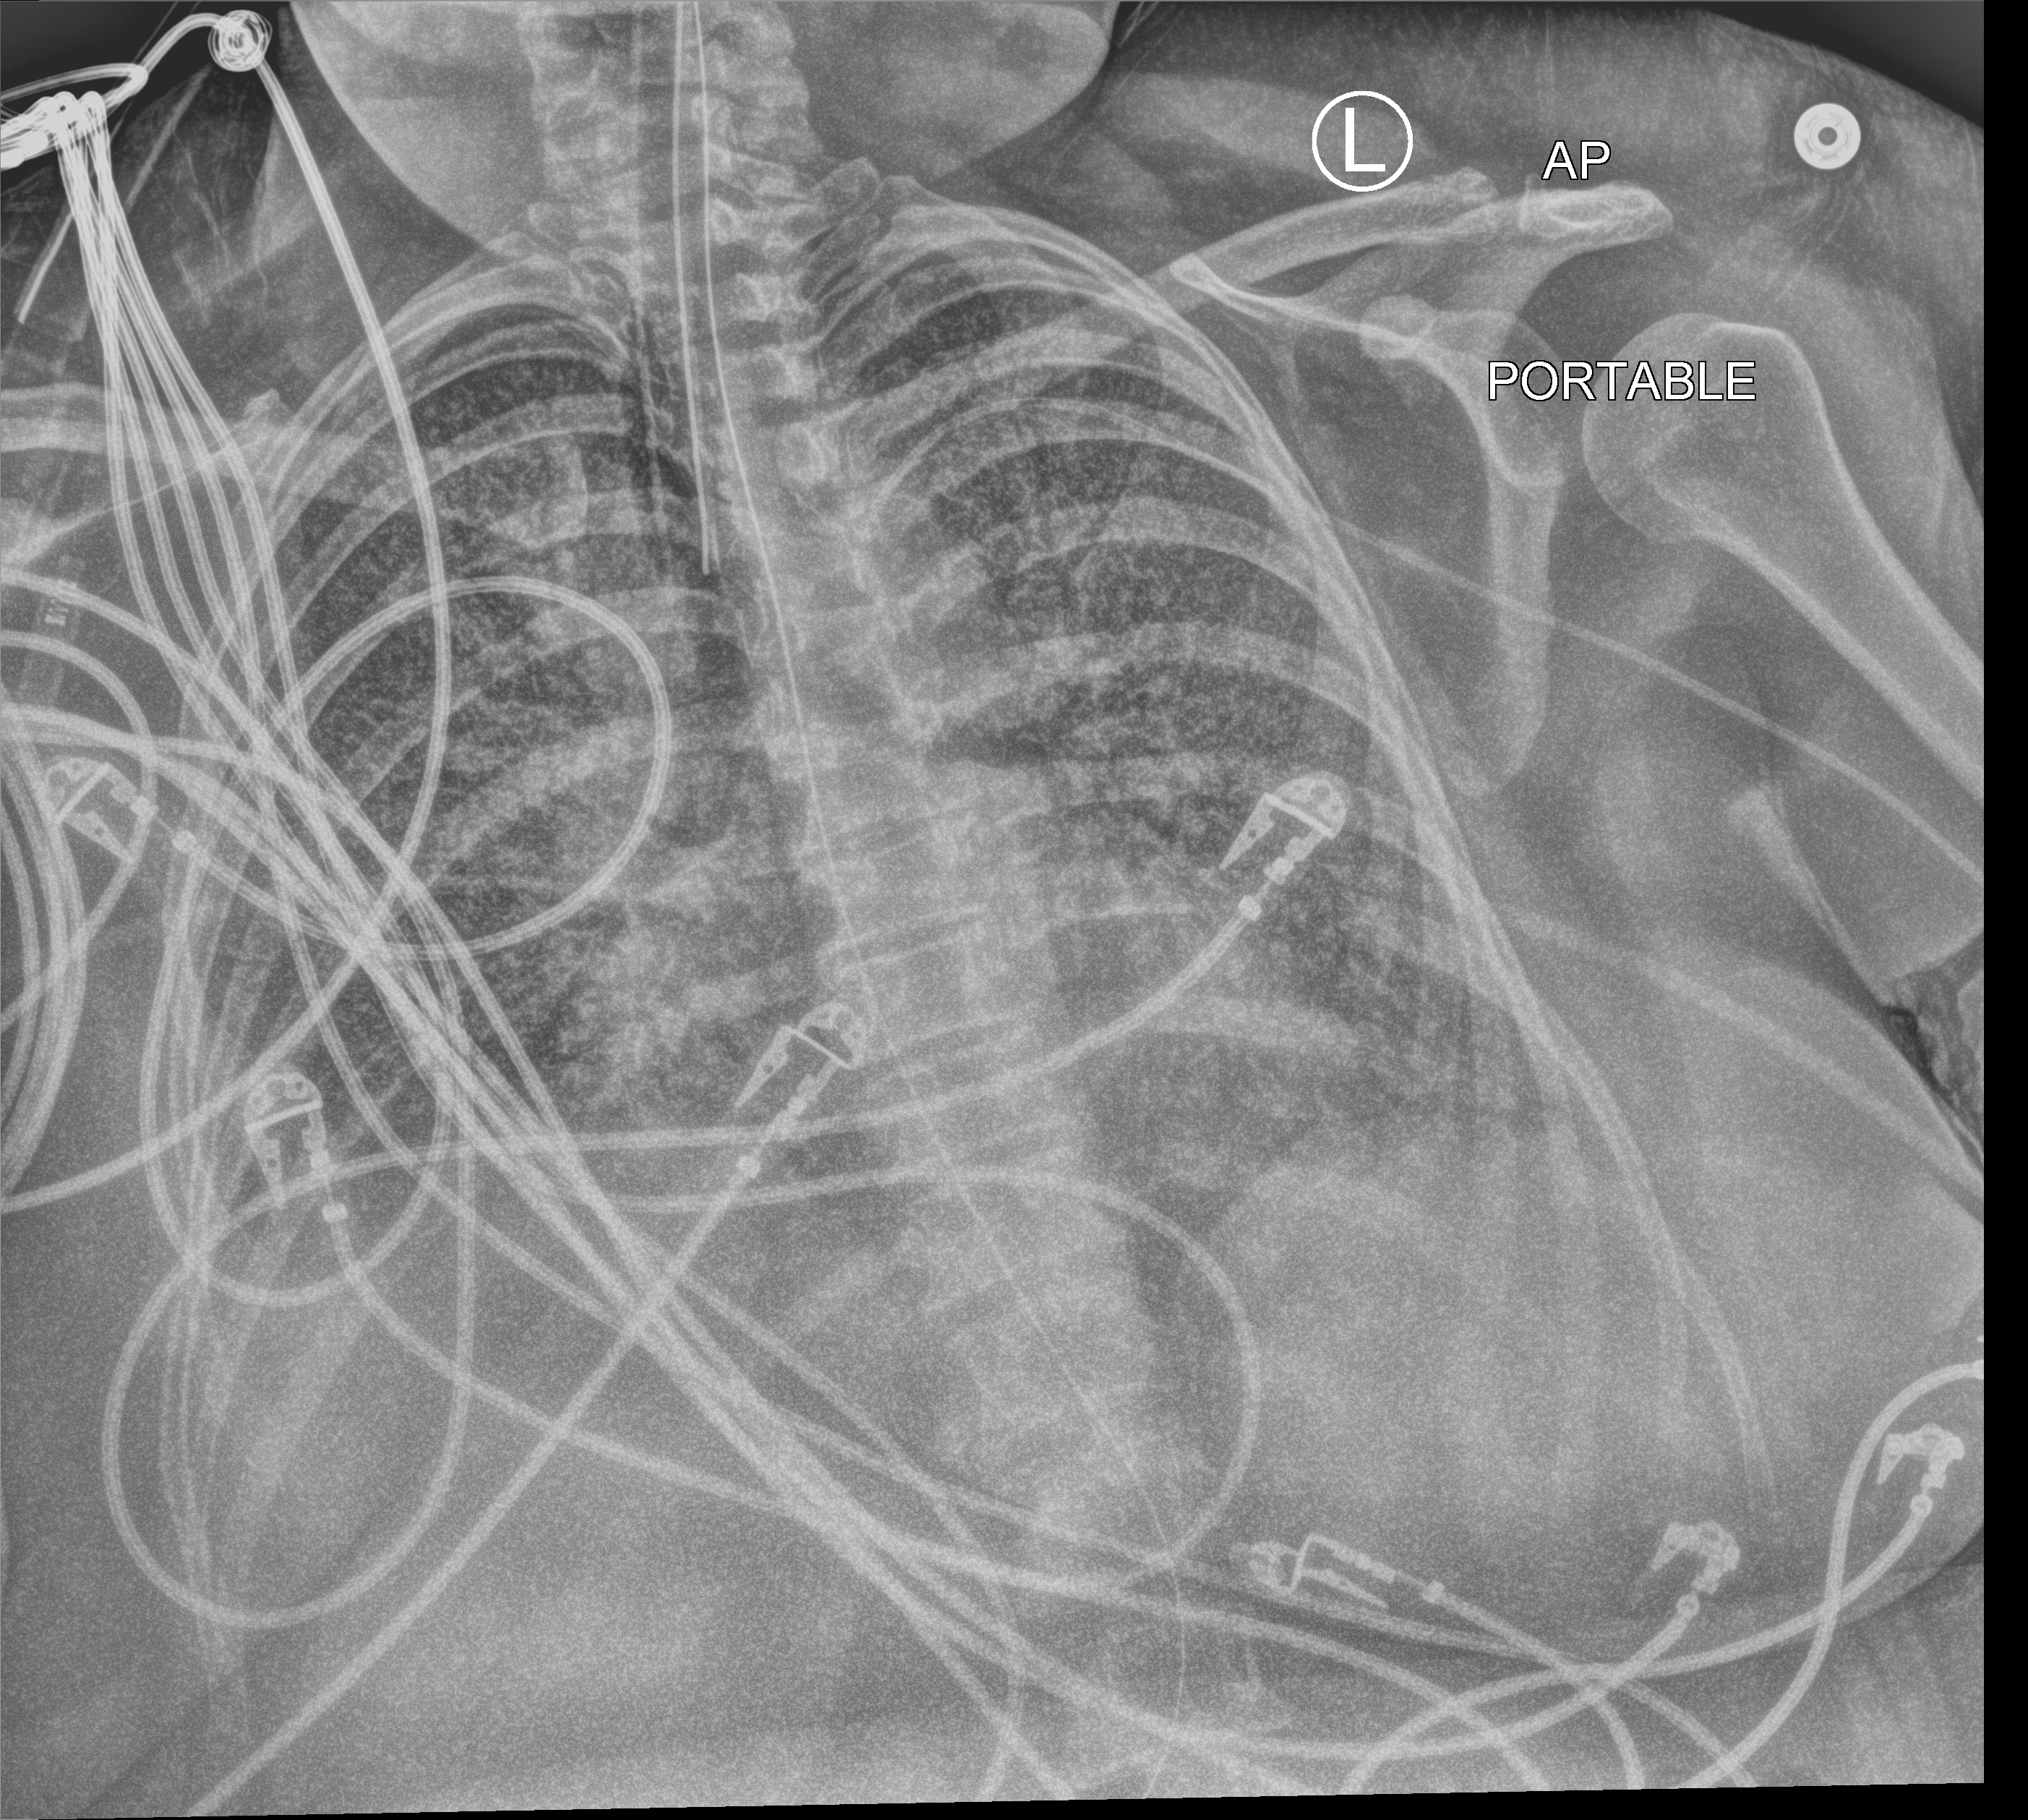
Chest X-ray (portable). Patient hospitalised with COVID-19; female, aged 18–59 years.
From the hospital-stay record, not from the radiograph (when in the stay this image was taken is not recorded): mechanically ventilated during this hospital stay: yes; admitted to intensive care during this hospital stay: yes.